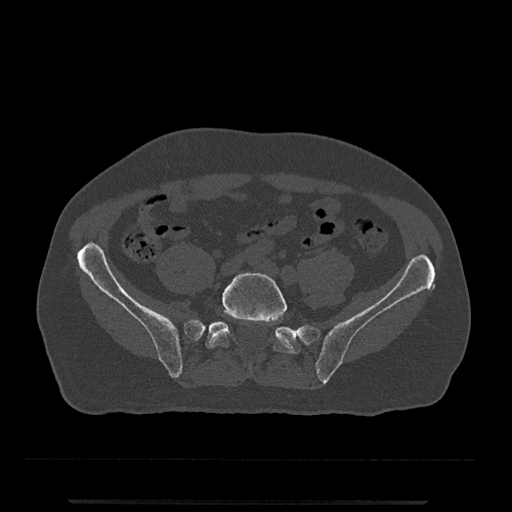
CT including the spine, one axial slice. Reconstruction kernel Br40s/3. 120 kVp. Bone window (W 1800 / L 400 HU). 0.5 mm slice thickness. 512 × 512 image matrix. Male patient, age 63 years. From the clinical record (not read from this slice): primary cancer: prostate.
Annotated regions visible in this slice (semi-automatically segmented with operator editing):
- L5 vertebra: bounding box [x1, y1, x2, y2] px = [209, 272, 292, 366]